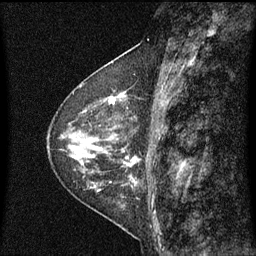
Breast MRI (dynamic contrast-enhanced), one sagittal slice; slice 27 of 60 in the series (ordered by position); dynamic contrast-enhanced series, image 2 of 3 at this slice position (ordered by acquisition); 1.5 T; TE 4.2 ms, TR 8 ms; 2 mm slice thickness; 256 × 256 image matrix, field of view 200 × 200 mm. Female patient, age 48 years.
Annotated regions visible in this slice (semi-automatic segmentation, software-assisted and operator-edited):
- analysis volume of interest (the breast-tissue region the enhancement analysis was run in; not a lesion): box from (x=103, y=74) to (x=145, y=139) px
- tumour enhancement mask (voxels above the 70 % enhancement threshold inside the analysis volume of interest): (x=108, y=88)–(x=136, y=117)